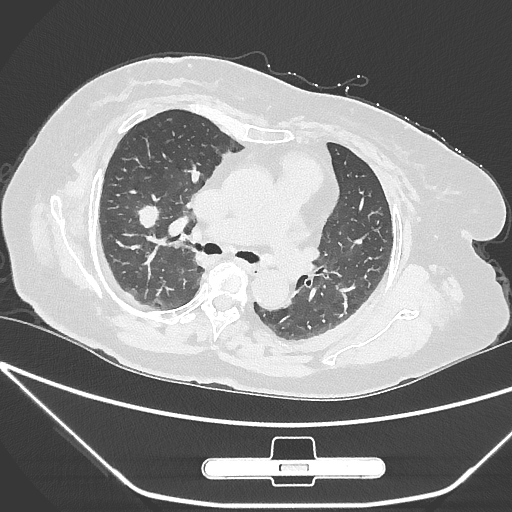
Chest CT, one axial slice. Slice 163 of 245 in the series (ordered by position). 120 kVp. Lung window (W 1500 / L -600 HU). 1 mm slice thickness. 512 × 512 image matrix. Female patient, age 65 years. From the clinical record (not read from this slice): clinical TNM (as recorded): T1c N0 M0; histopathological grade: G3.
Annotated regions visible in this slice (rectangle marked by the reading radiologist):
- lung tumour (recorded histology: adenocarcinoma): bounding box (x1, y1, x2, y2) in pixels: (129, 193, 171, 245)